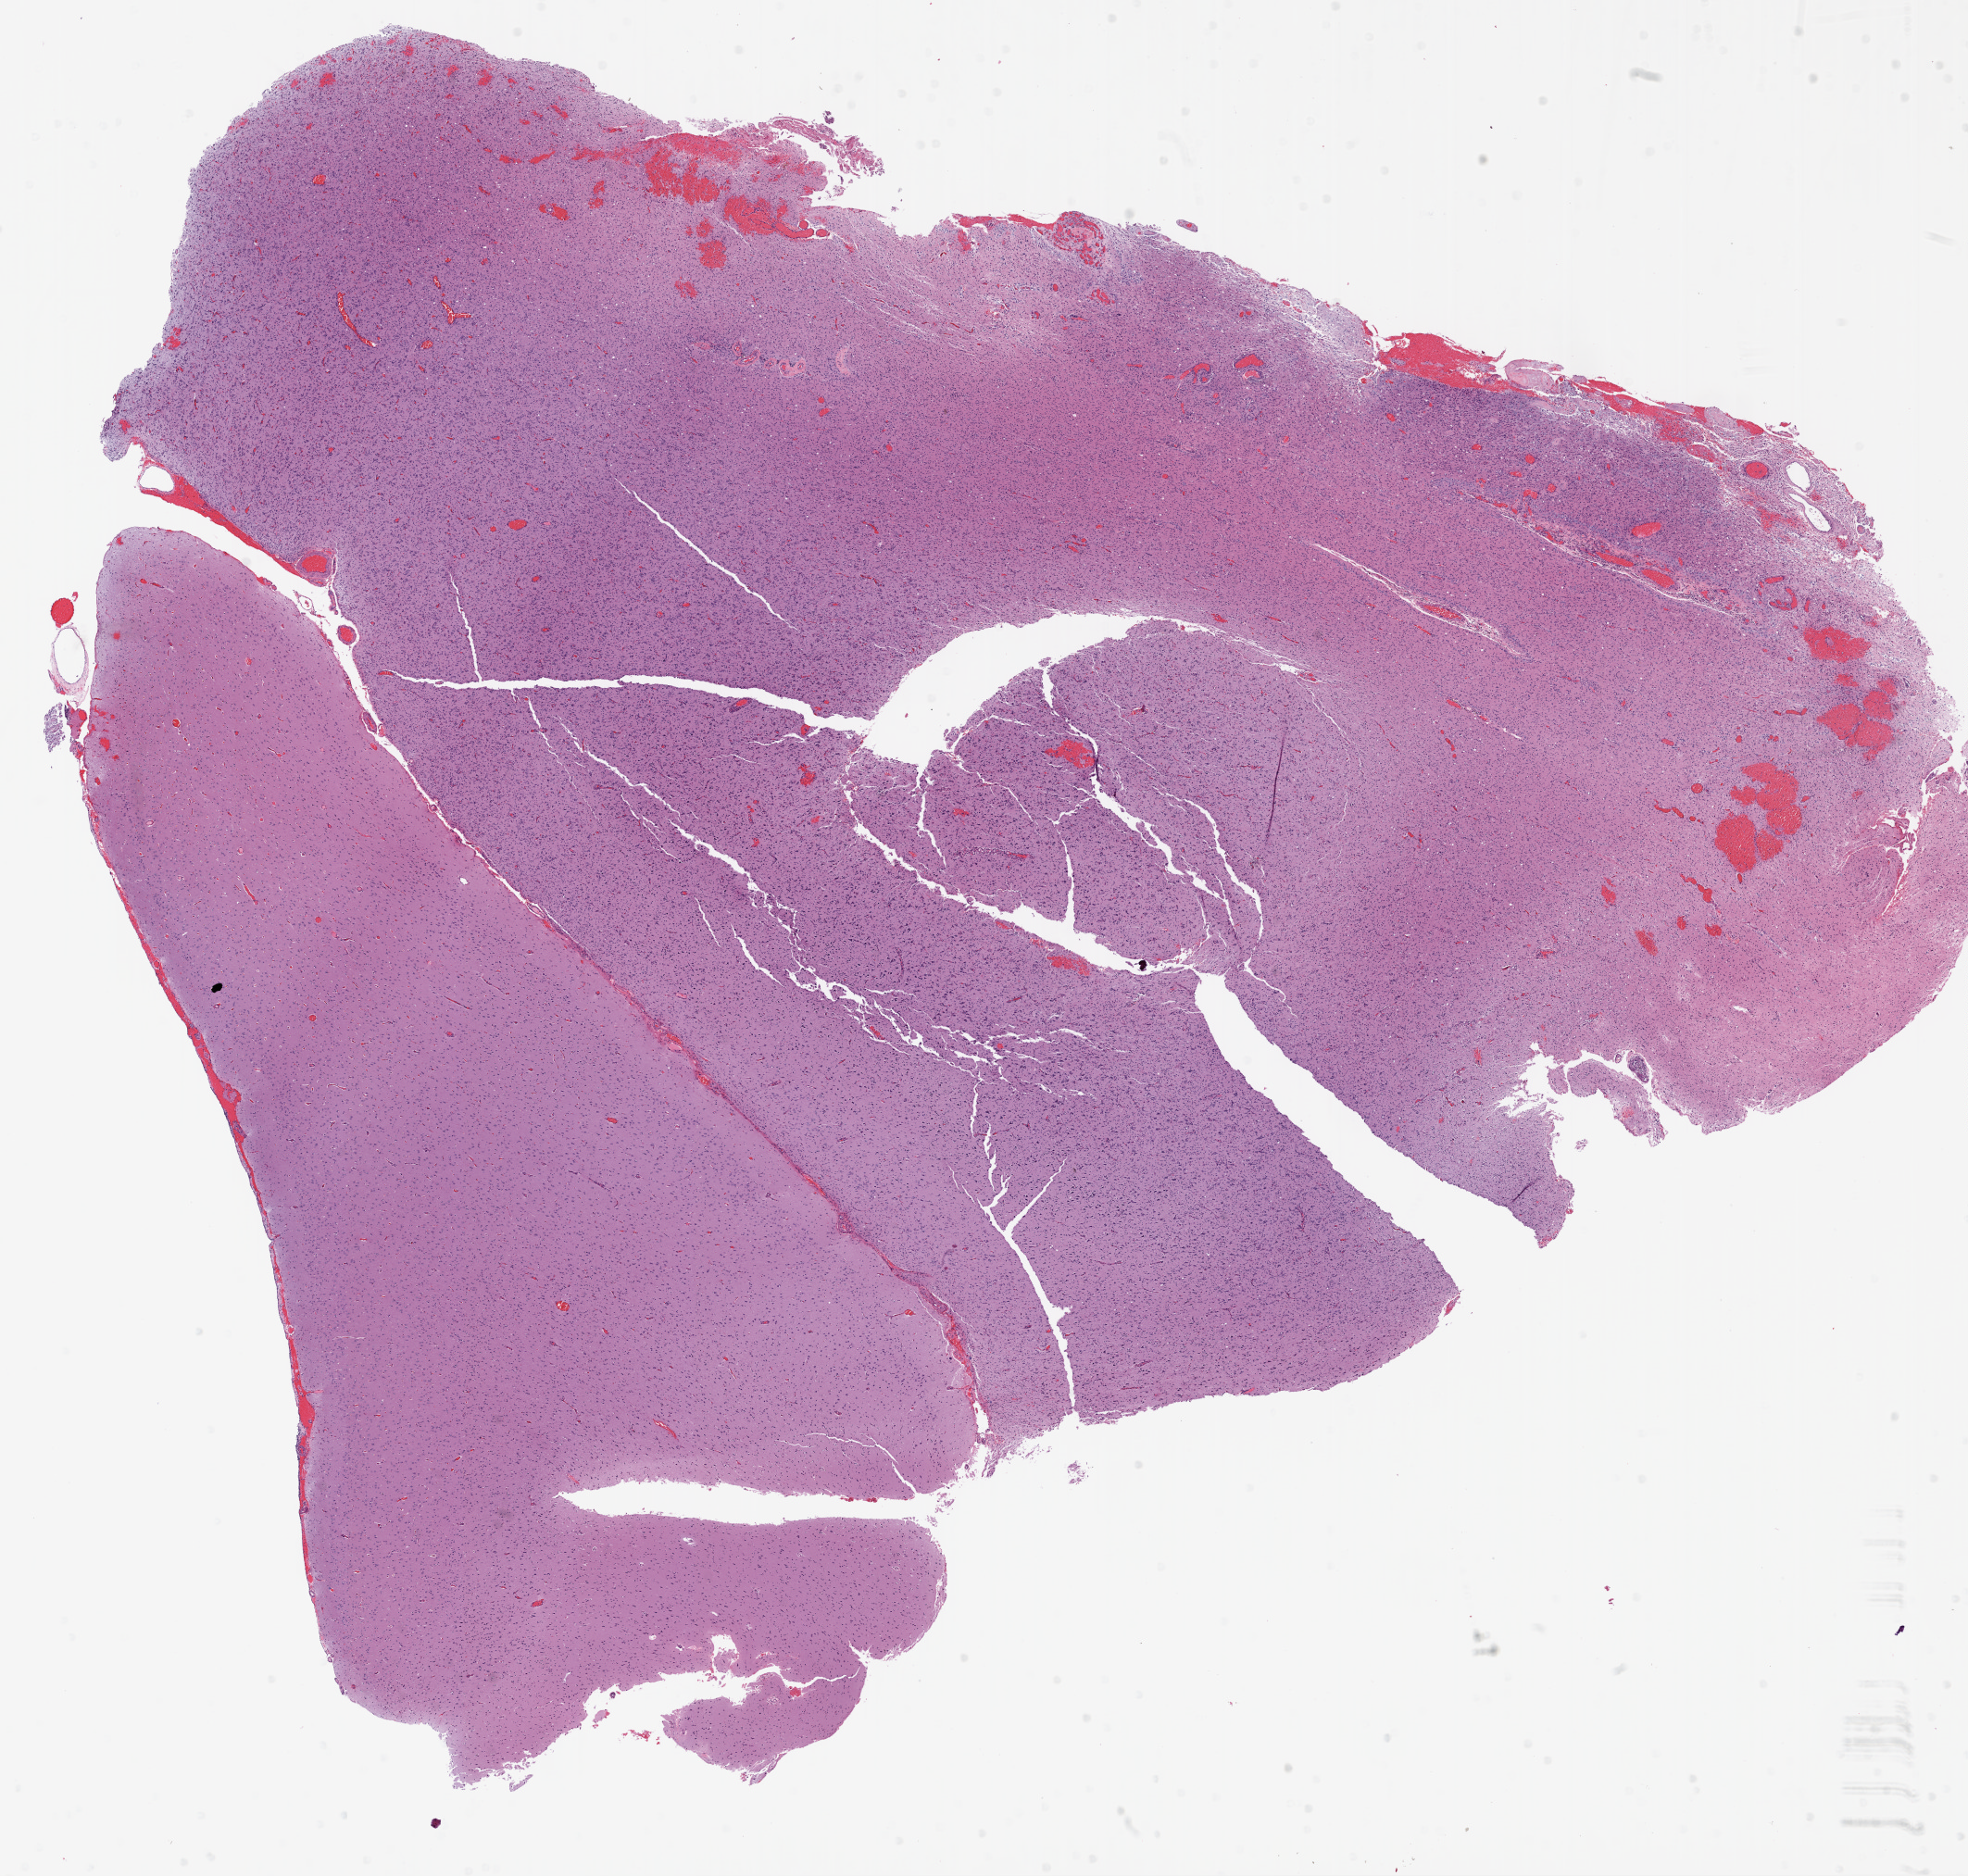
H&E-stained whole-slide image — a low-resolution overview of the entire scanned area, about 17.1 x 16.3 mm, formalin-fixed paraffin-embedded (FFPE) diagnostic section, sample: primary tumour, brain. Male, age 57 years at initial diagnosis.
Diagnosis: Glioblastoma.